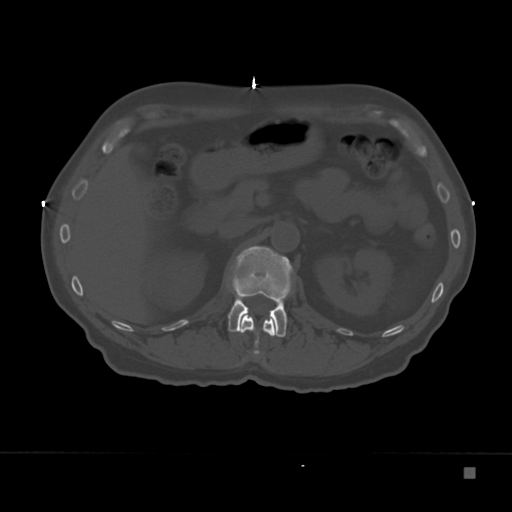
CT including the spine, one axial slice; slice 118 of 332 in the series (ordered by position); 120 kVp; bone window (W 1800 / L 400 HU); 1.5 mm slice thickness; 512 × 512 image matrix, field of view 389 × 389 mm. Patient: male, 72 years. From the clinical record (not read from this slice): primary cancer: skeletal.
Annotated regions visible in this slice (semi-automatically segmented with operator editing):
- L1 vertebra: bounding box (x1, y1, x2, y2) in pixels: (228, 246, 292, 337)
- T12 vertebra: (241, 315, 275, 355)